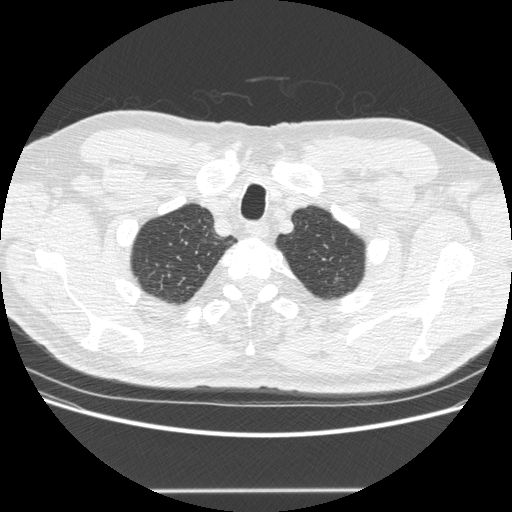
Chest CT (low-dose screening protocol), one axial image, second annual screen, lung window (W 1500 / L -600 HU), 1.25 mm slice thickness. Male participant, aged 69 years at enrolment.
- Expert-annotated lung lesion, bounding box <312,264,345,294> (left, top, right, bottom; pixels).
- Screening reader's record for this exam: no non-calcified nodule ≥4 mm recorded.
- Later outcome: lung cancer diagnosed 485 days after this screen (after the third annual screen) — adenocarcinoma, NOS, left upper lobe, moderately differentiated (G2), stage IA (AJCC 6th edition), 10 mm at pathology.